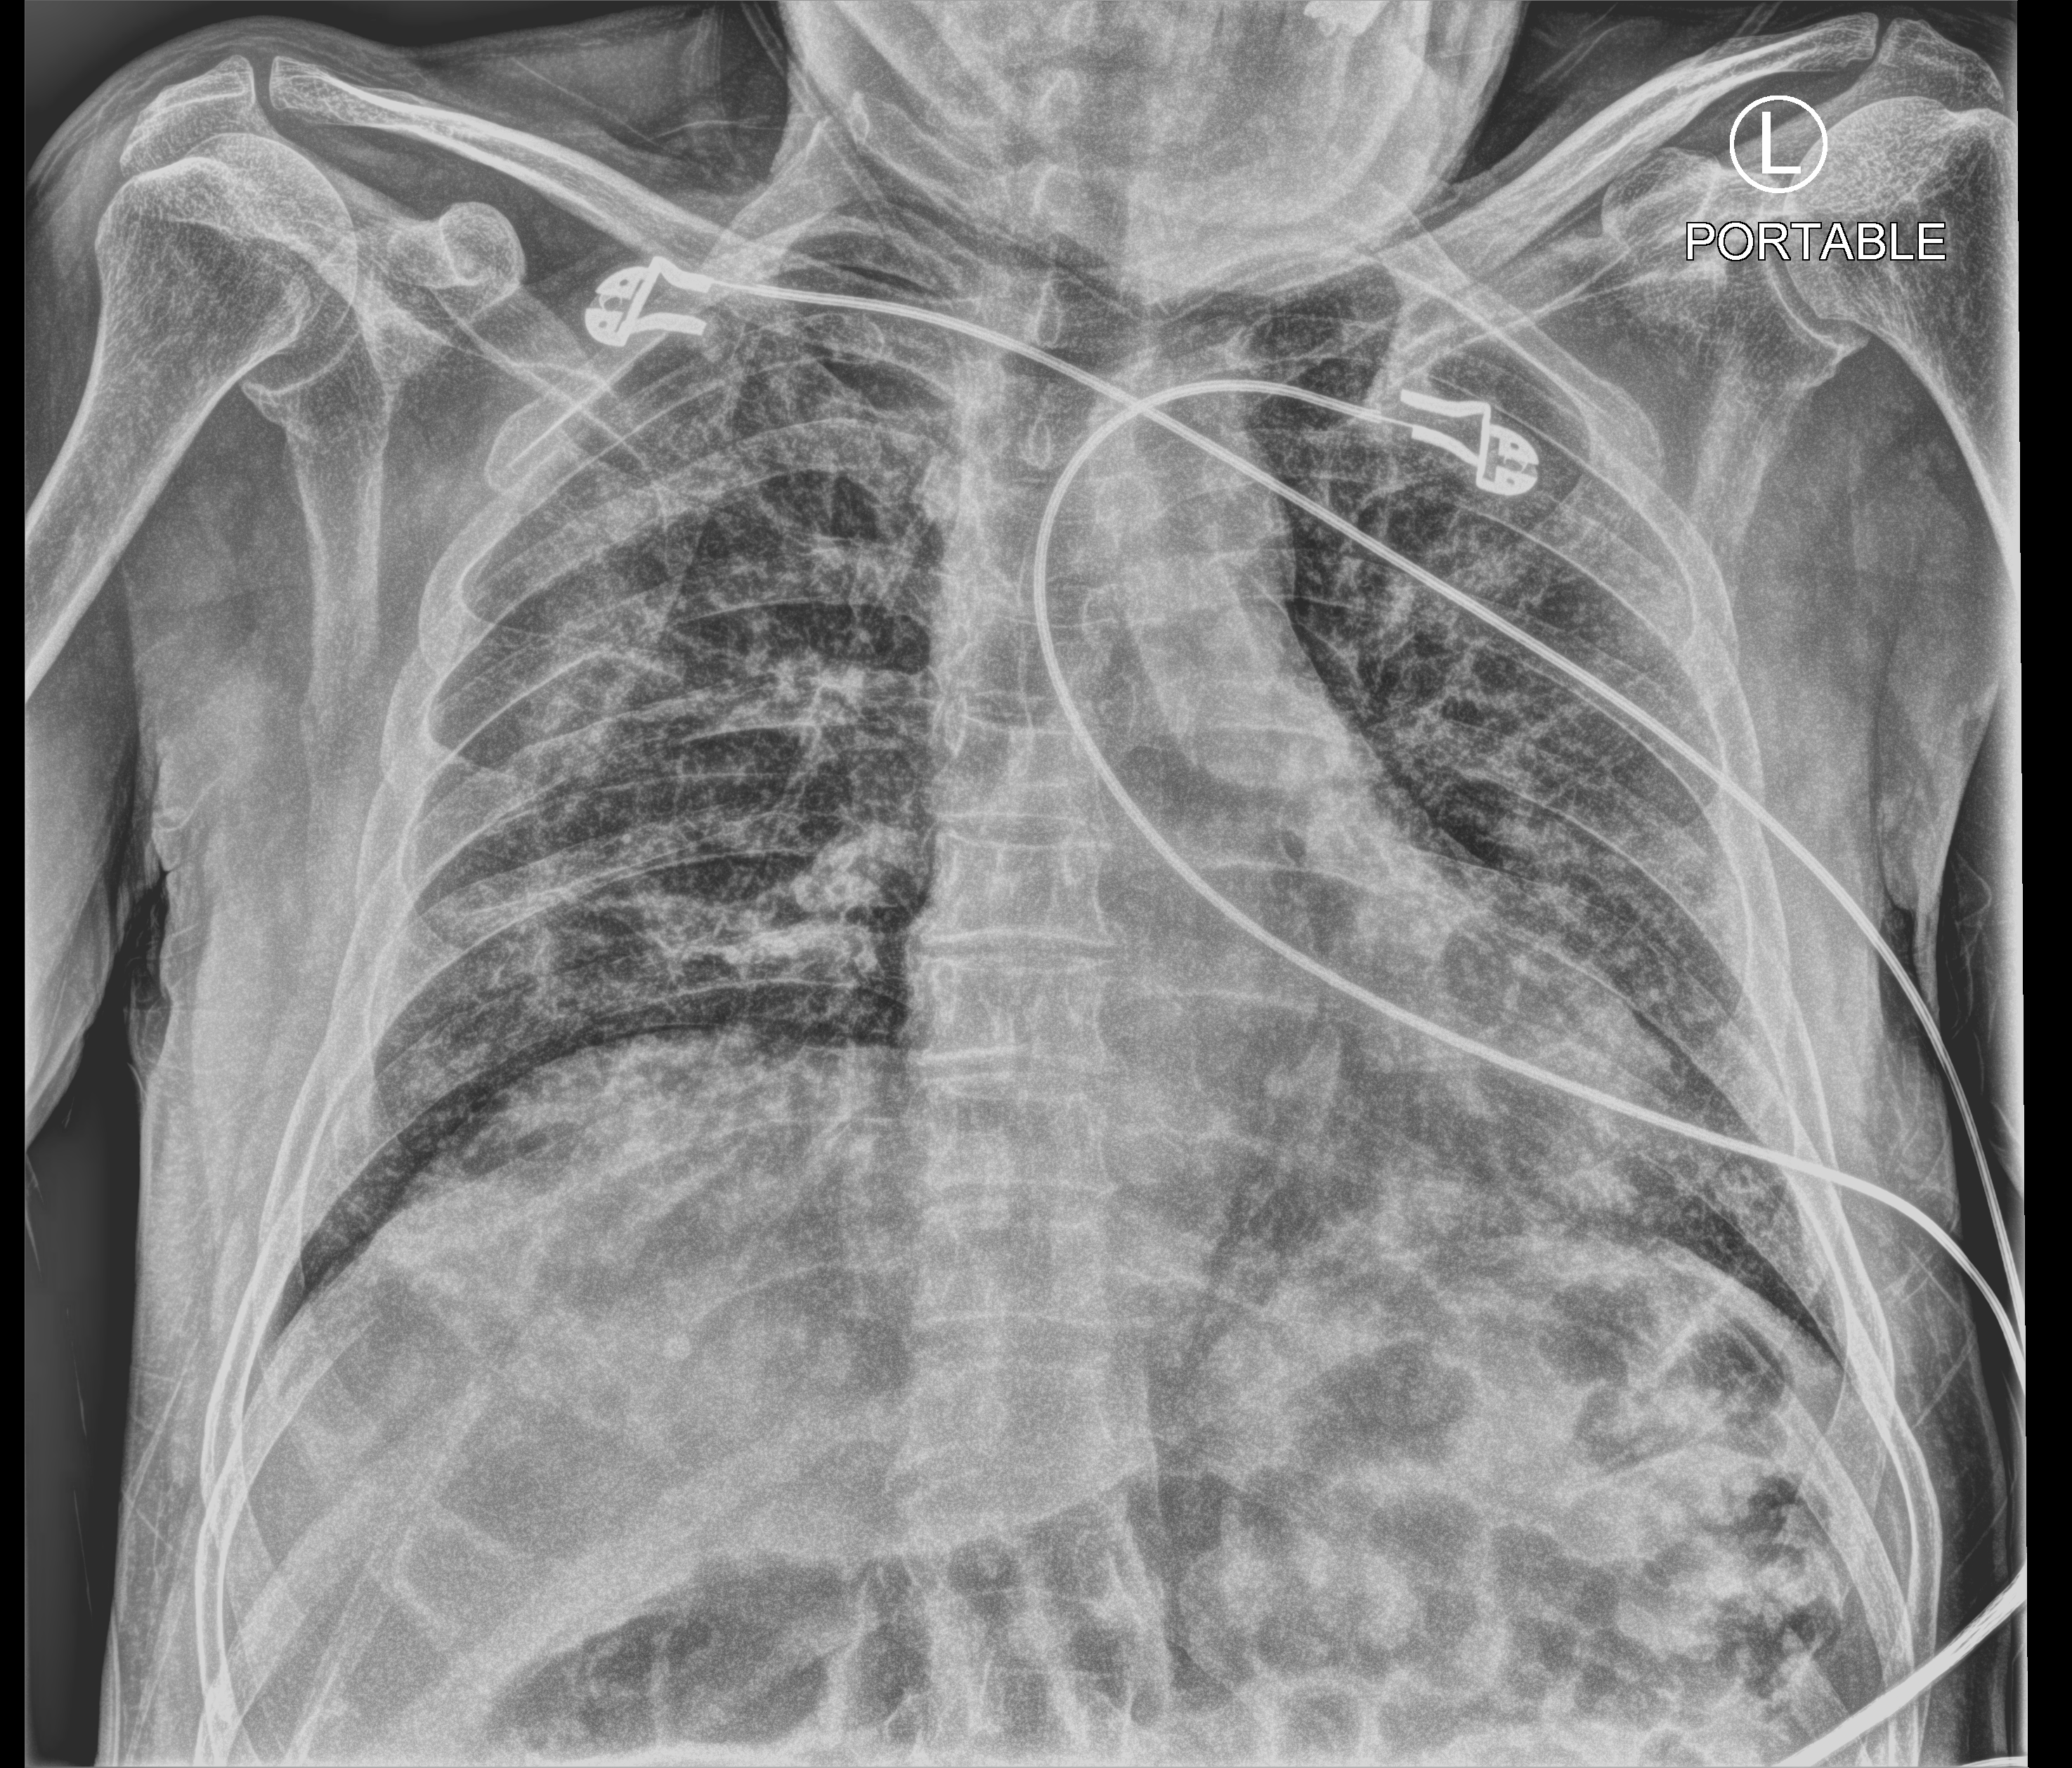
Bedside chest radiograph (computed radiography), anteroposterior (AP) projection. Patient hospitalised with COVID-19; male, aged 60–74 years.
From the hospital-stay record, not from the radiograph (when in the stay this image was taken is not recorded):
- admitted to intensive care during this hospital stay: no